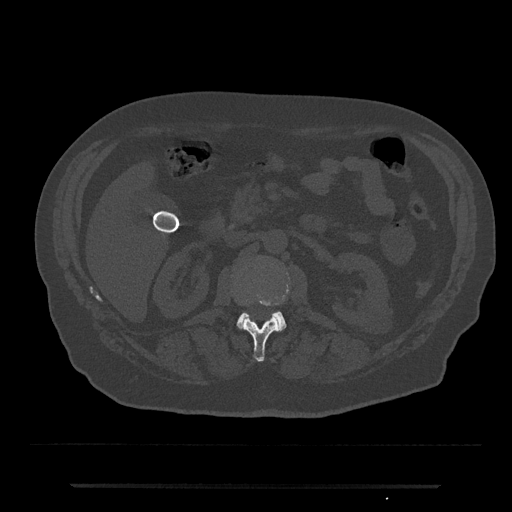
CT including the spine, one axial slice; reconstruction kernel Br40s/3; bone window (W 1800 / L 400 HU); 0.5 mm slice thickness; 512 × 512 image matrix, field of view 434 × 434 mm. Male patient, age 80 years. Case-level facts recorded for this patient, not image findings: primary cancer: prostate.
Annotated regions visible in this slice (semi-automatically segmented with operator editing):
- L1 vertebra: bounding box (x1, y1, x2, y2) in pixels: (243, 300, 280, 362)
- L2 vertebra: (236, 311, 287, 332)